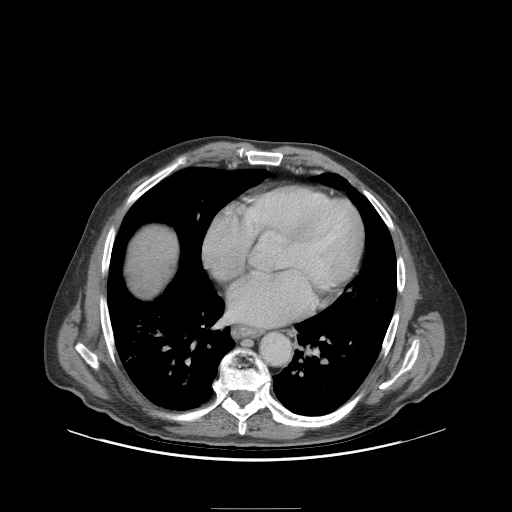
Contrast-enhanced abdominal CT (liver protocol), one axial slice. Position 99 of 105 along the scan axis. Reconstruction kernel STANDARD. 140 kVp. Soft-tissue window (W 400 / L 40 HU). 2.5 mm slice thickness. 512 × 512 image matrix, field of view 440 × 440 mm. From the clinical record (not read from this slice): diagnosis: hepatocellular carcinoma (patient treated with transarterial chemoembolisation; whether this scan precedes or follows treatment is not stated here); TNM stage (as recorded): Stage-I.
Annotated regions visible in this slice (semi-automatic segmentation, software-assisted and operator-edited):
- liver parenchyma outside the tumour (the mass and vessels are separate outlines, so this box may not span the whole liver): box from (x=126, y=226) to (x=176, y=296) px